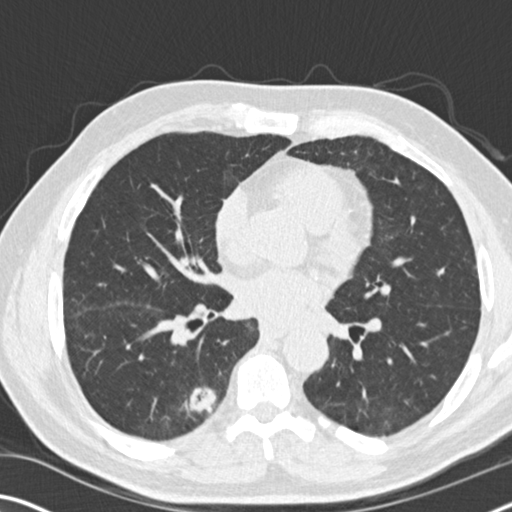
Low-dose screening chest CT, one axial slice. Position 82 of 169 along the scan axis. Reconstruction kernel B30f. 120 kVp. Lung window (W 1500 / L -600 HU). 2 mm slice thickness. 512 × 512 image matrix, field of view 340 × 340 mm.
Annotated regions visible in this slice (outlined manually by an expert reader):
- lesion 1 (tumor, lower lobe of right lung): bounding box [x1, y1, x2, y2] px = [189, 386, 216, 414]